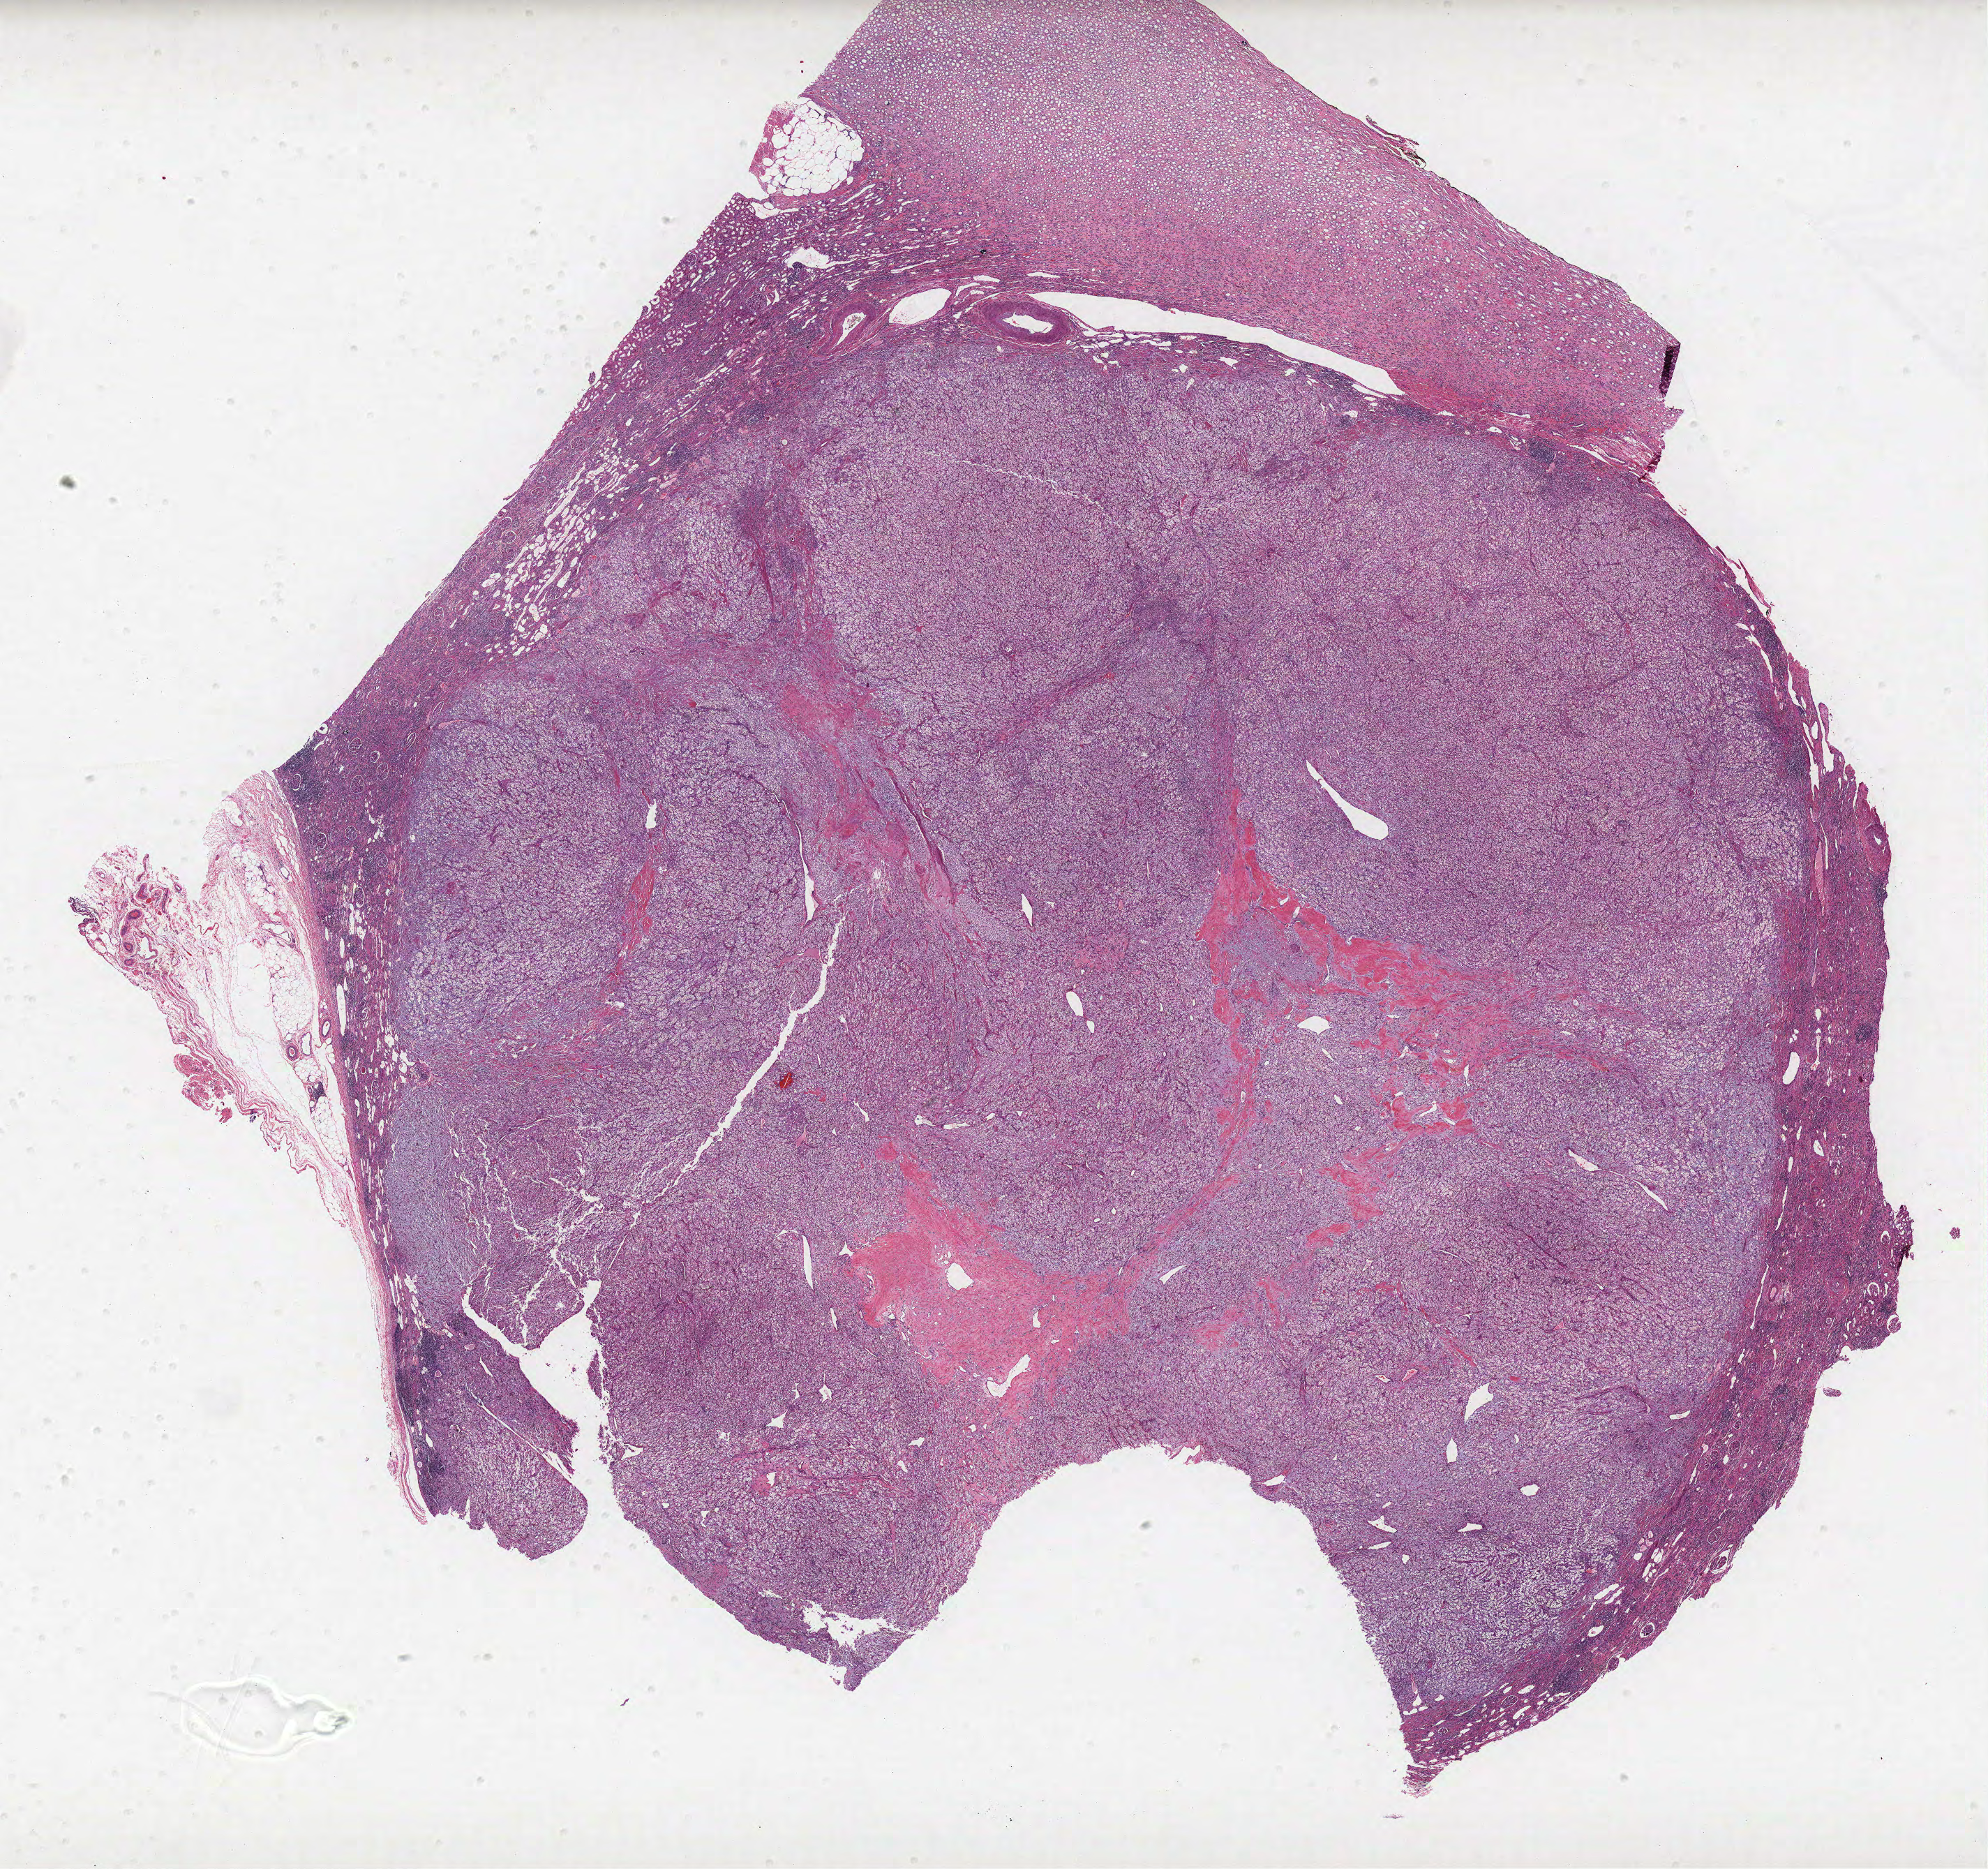
H&E whole-slide image, whole scanned area (about 22.8 x 21.4 mm) shown as a low-resolution overview; formalin-fixed paraffin-embedded (FFPE) diagnostic section; primary tumour sample from the kidney. Male, age 75 years at initial diagnosis. Histologic grade: G3 (poorly differentiated).
Lymph nodes positive (case pathology): 0 of 4 examined. AJCC pathologic stage: I. Laterality: right. Diagnosis: Clear cell adenocarcinoma, NOS.